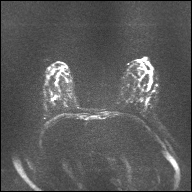
Breast MRI, one axial slice. Slice 20 of 32 in the series (ordered by position). Diffusion-weighted series; image 2 of 4 stored at this slice position (different b-values; order by instance number). 1.5 T. 4 mm slice thickness. 192 × 192 image matrix, field of view 360 × 360 mm. Female patient.
Outlined on this slice (outlined manually by an expert reader):
- tumour on diffusion-weighted imaging: box from (x=51, y=97) to (x=56, y=100) px